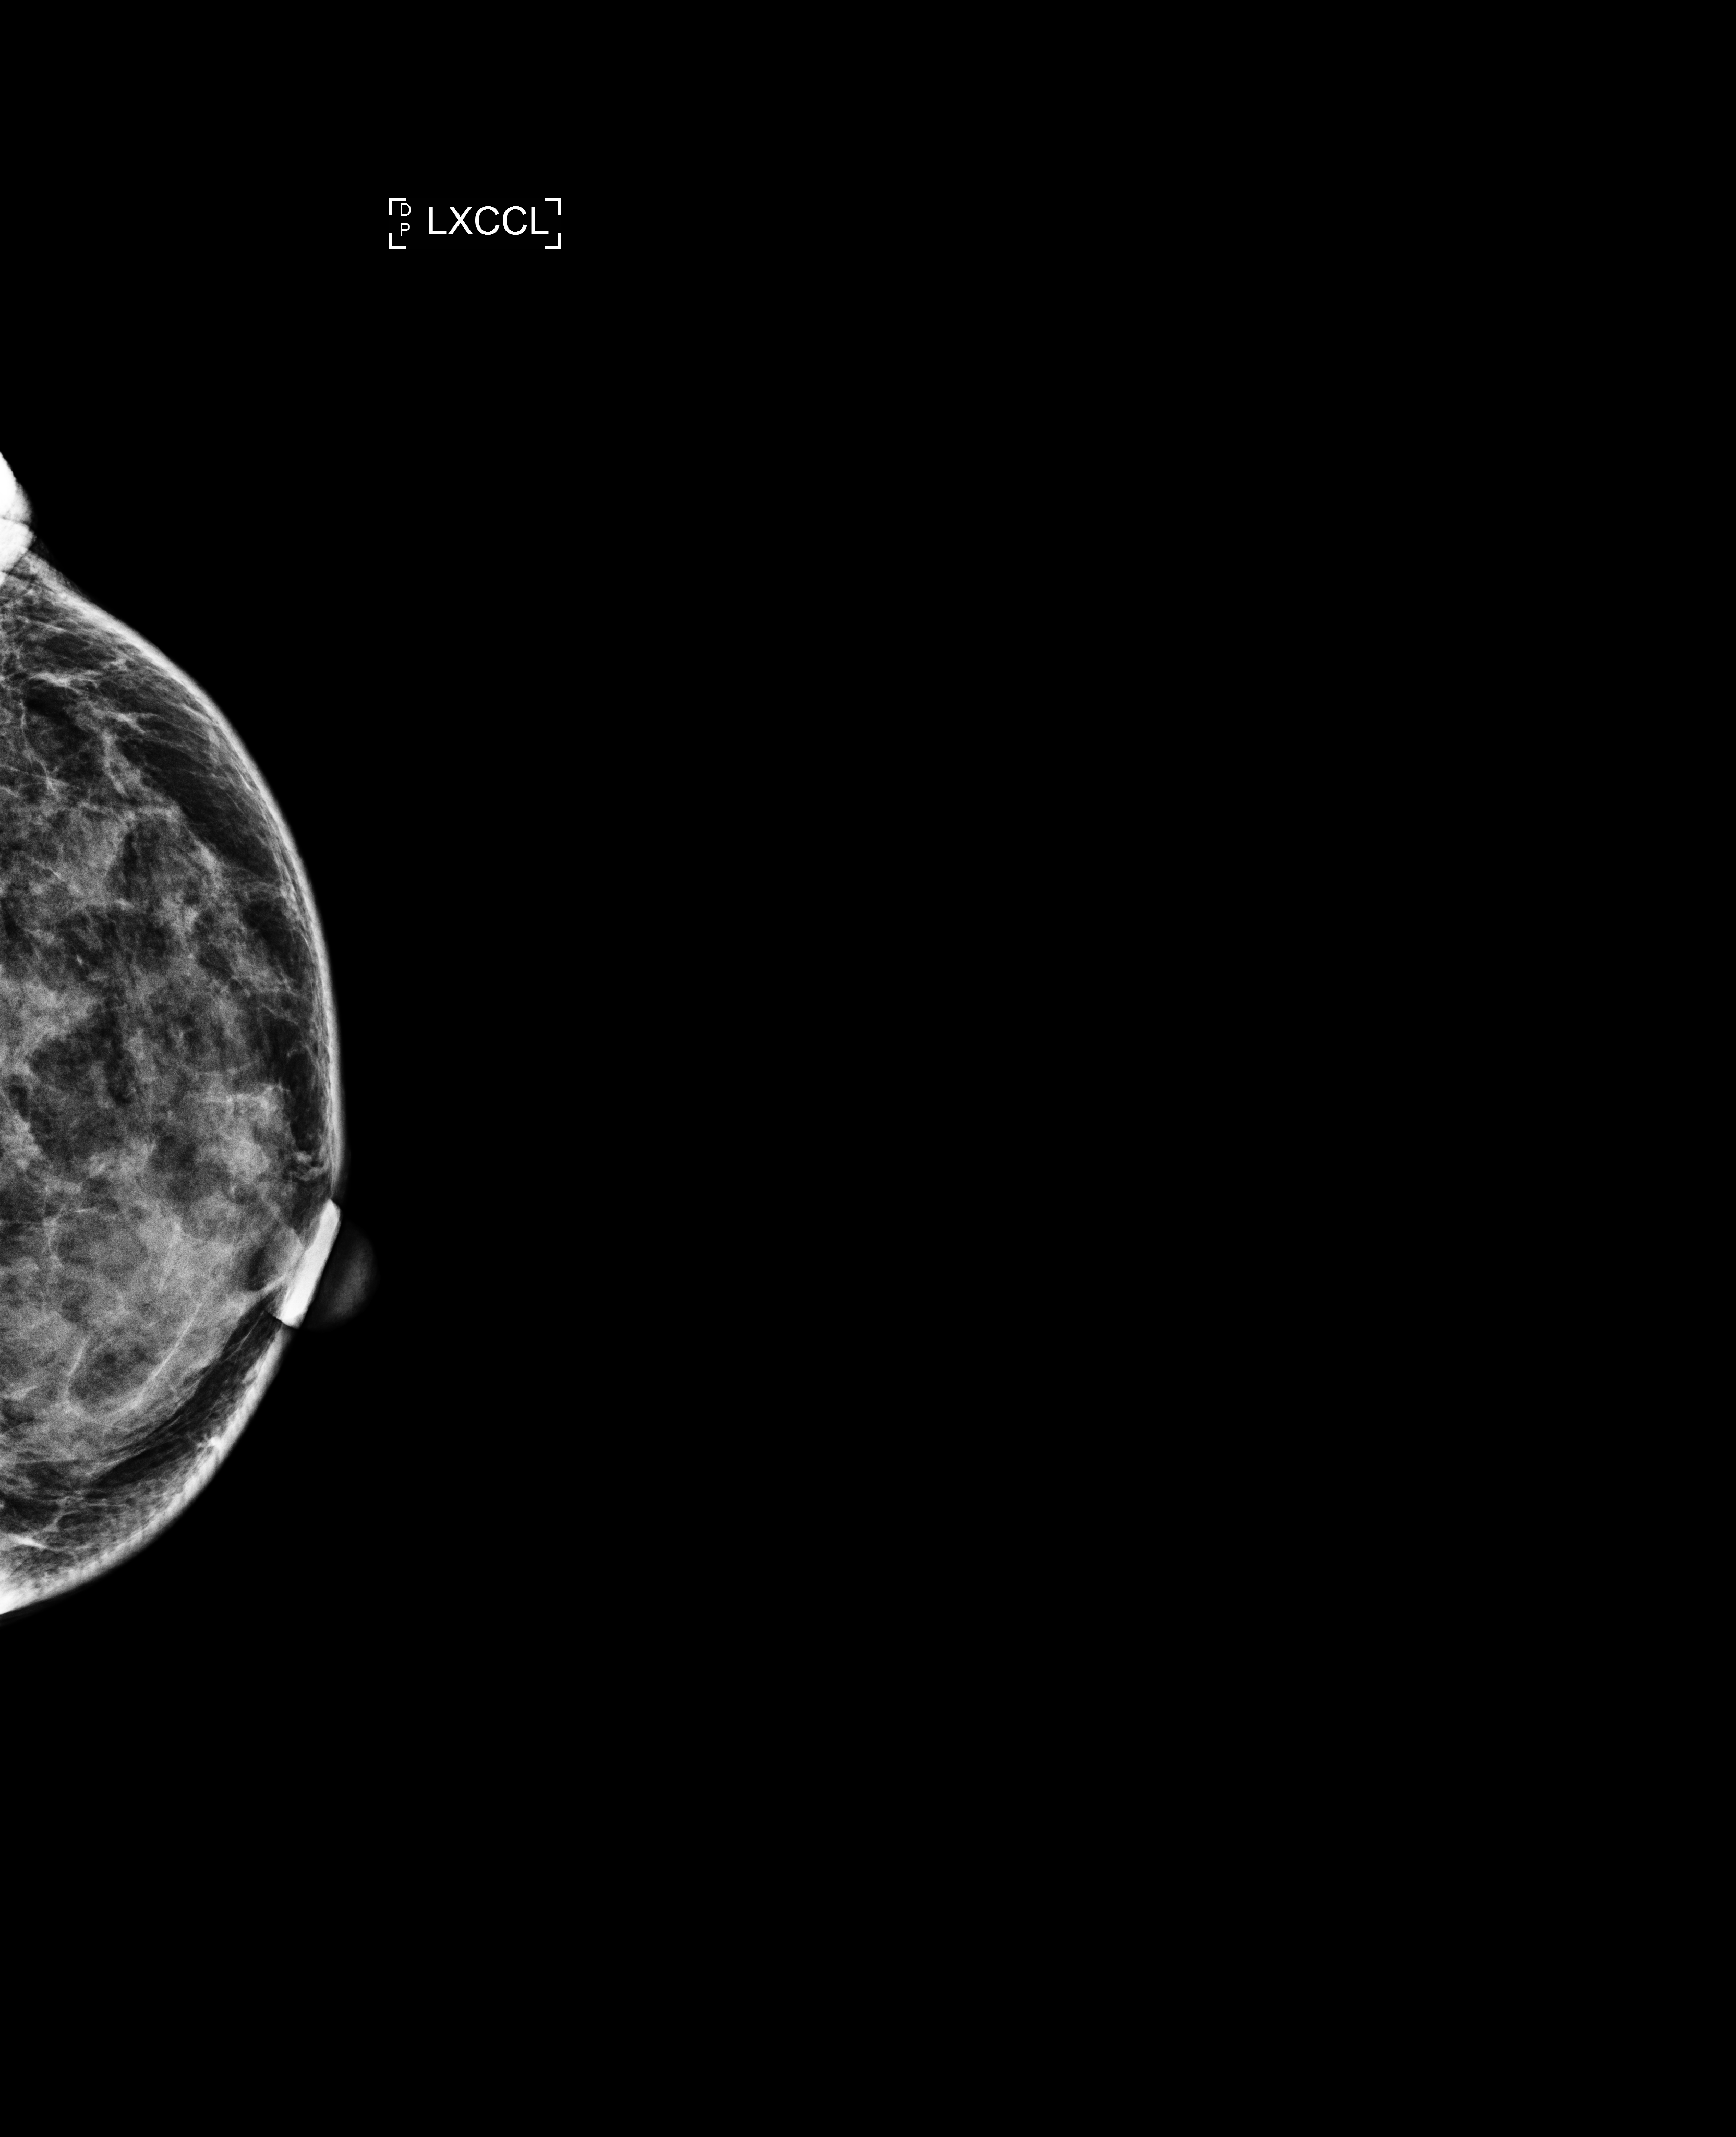
Screening examination; compressed breast thickness 36 mm. Female patient, age 60 years.
Image type: full-field digital mammogram. Breast: left. Projection: exaggerated CC view (lateral).